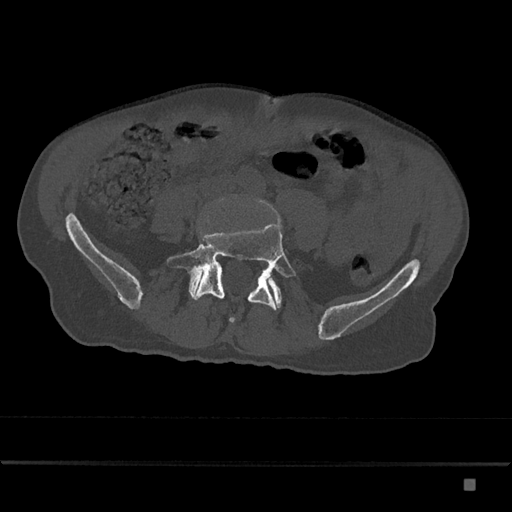
CT including the spine, one axial slice; position 281 of 797 along the scan axis; reconstruction kernel Br40s/3; 120 kVp; bone window (W 1800 / L 400 HU); 0.5 mm slice thickness; 512 × 512 image matrix, field of view 390 × 390 mm. Male patient, age 72 years. Case-level facts recorded for this patient, not image findings: primary cancer: prostate.
Annotated regions visible in this slice (semi-automatically segmented with operator editing):
- L5 vertebra: bounding box [x1, y1, x2, y2] px = [167, 222, 296, 323]